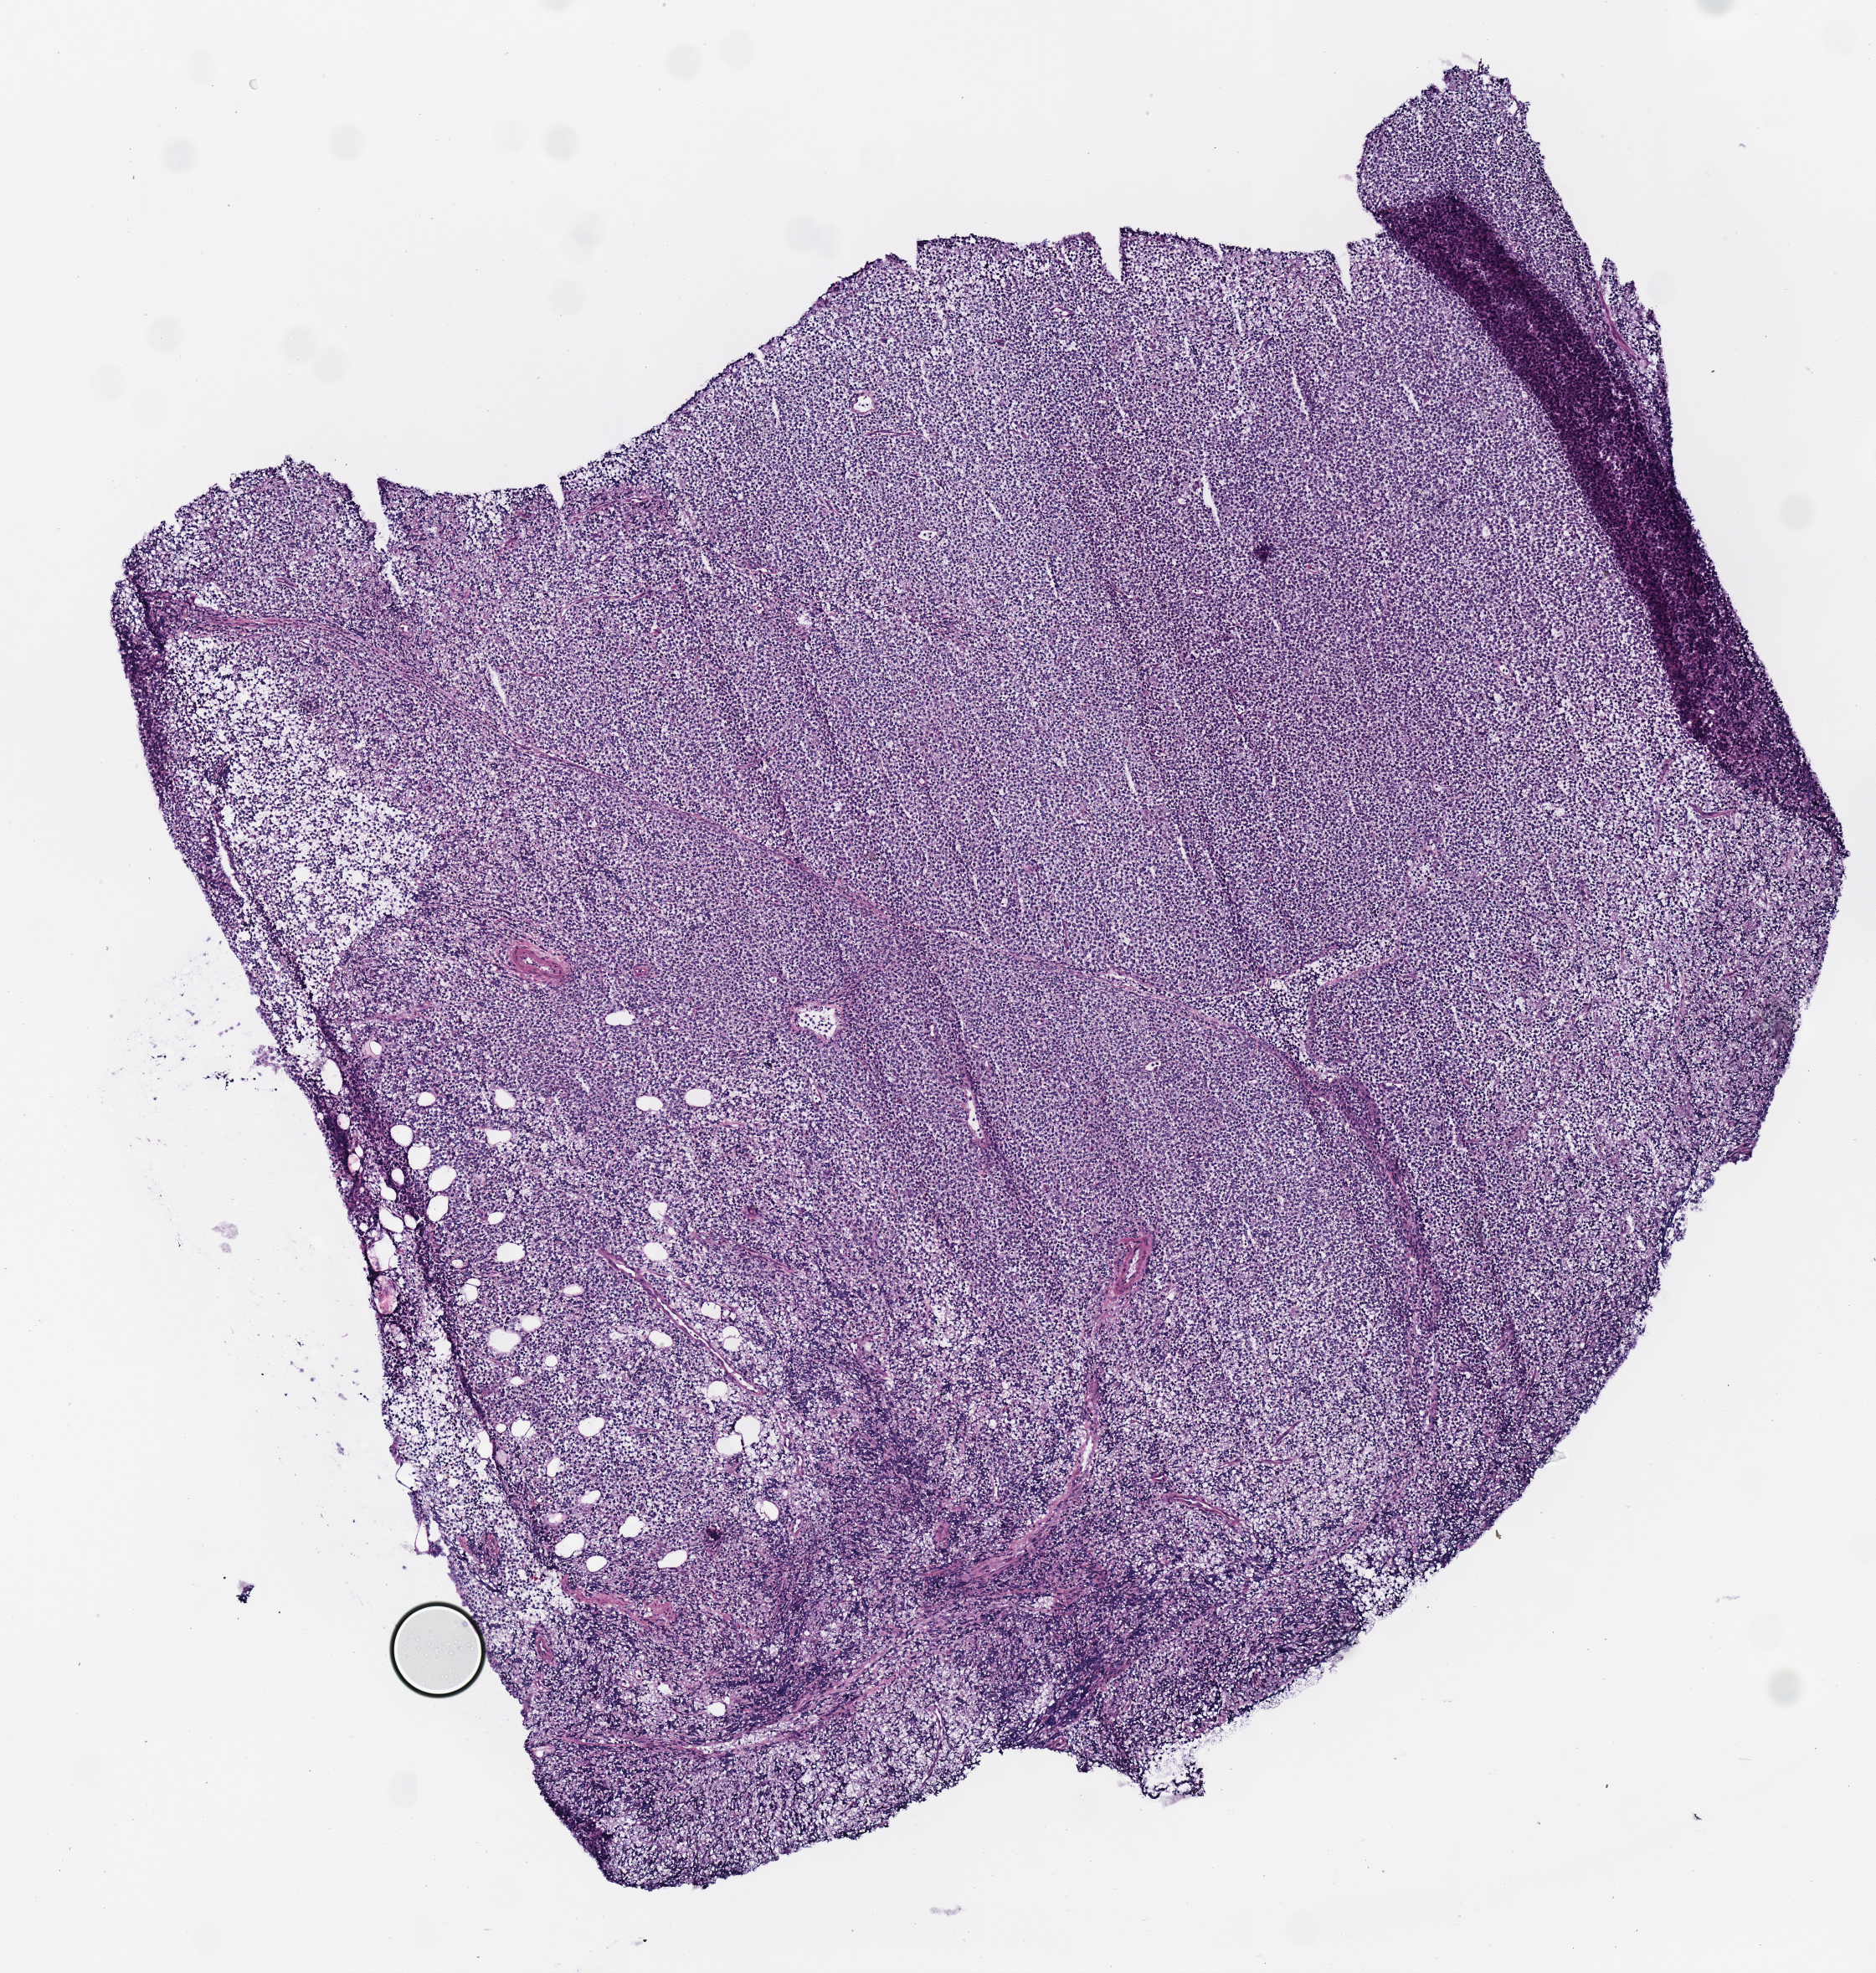
Digitized H&E tissue section (whole slide), shown as a low-resolution overview of the whole scanned area (about 4.4 x 4.6 mm, from a 40x scan). Frozen section from the top of the tissue portion. Primary tumour sample from the lymphoid tissue. Patient: female, age at initial diagnosis 38 years. Composition of this section per pathologist review: tumour cells 100%, tumour nuclei 95%, normal cells 0%, stromal cells 0%, necrosis 0%. Infiltration values recorded for this section: lymphocyte infiltration 2%, monocyte infiltration 0%, neutrophil infiltration 0%.
• pathologic diagnosis: Diffuse large B-cell lymphoma, NOS (lymph nodes of head, face and neck)